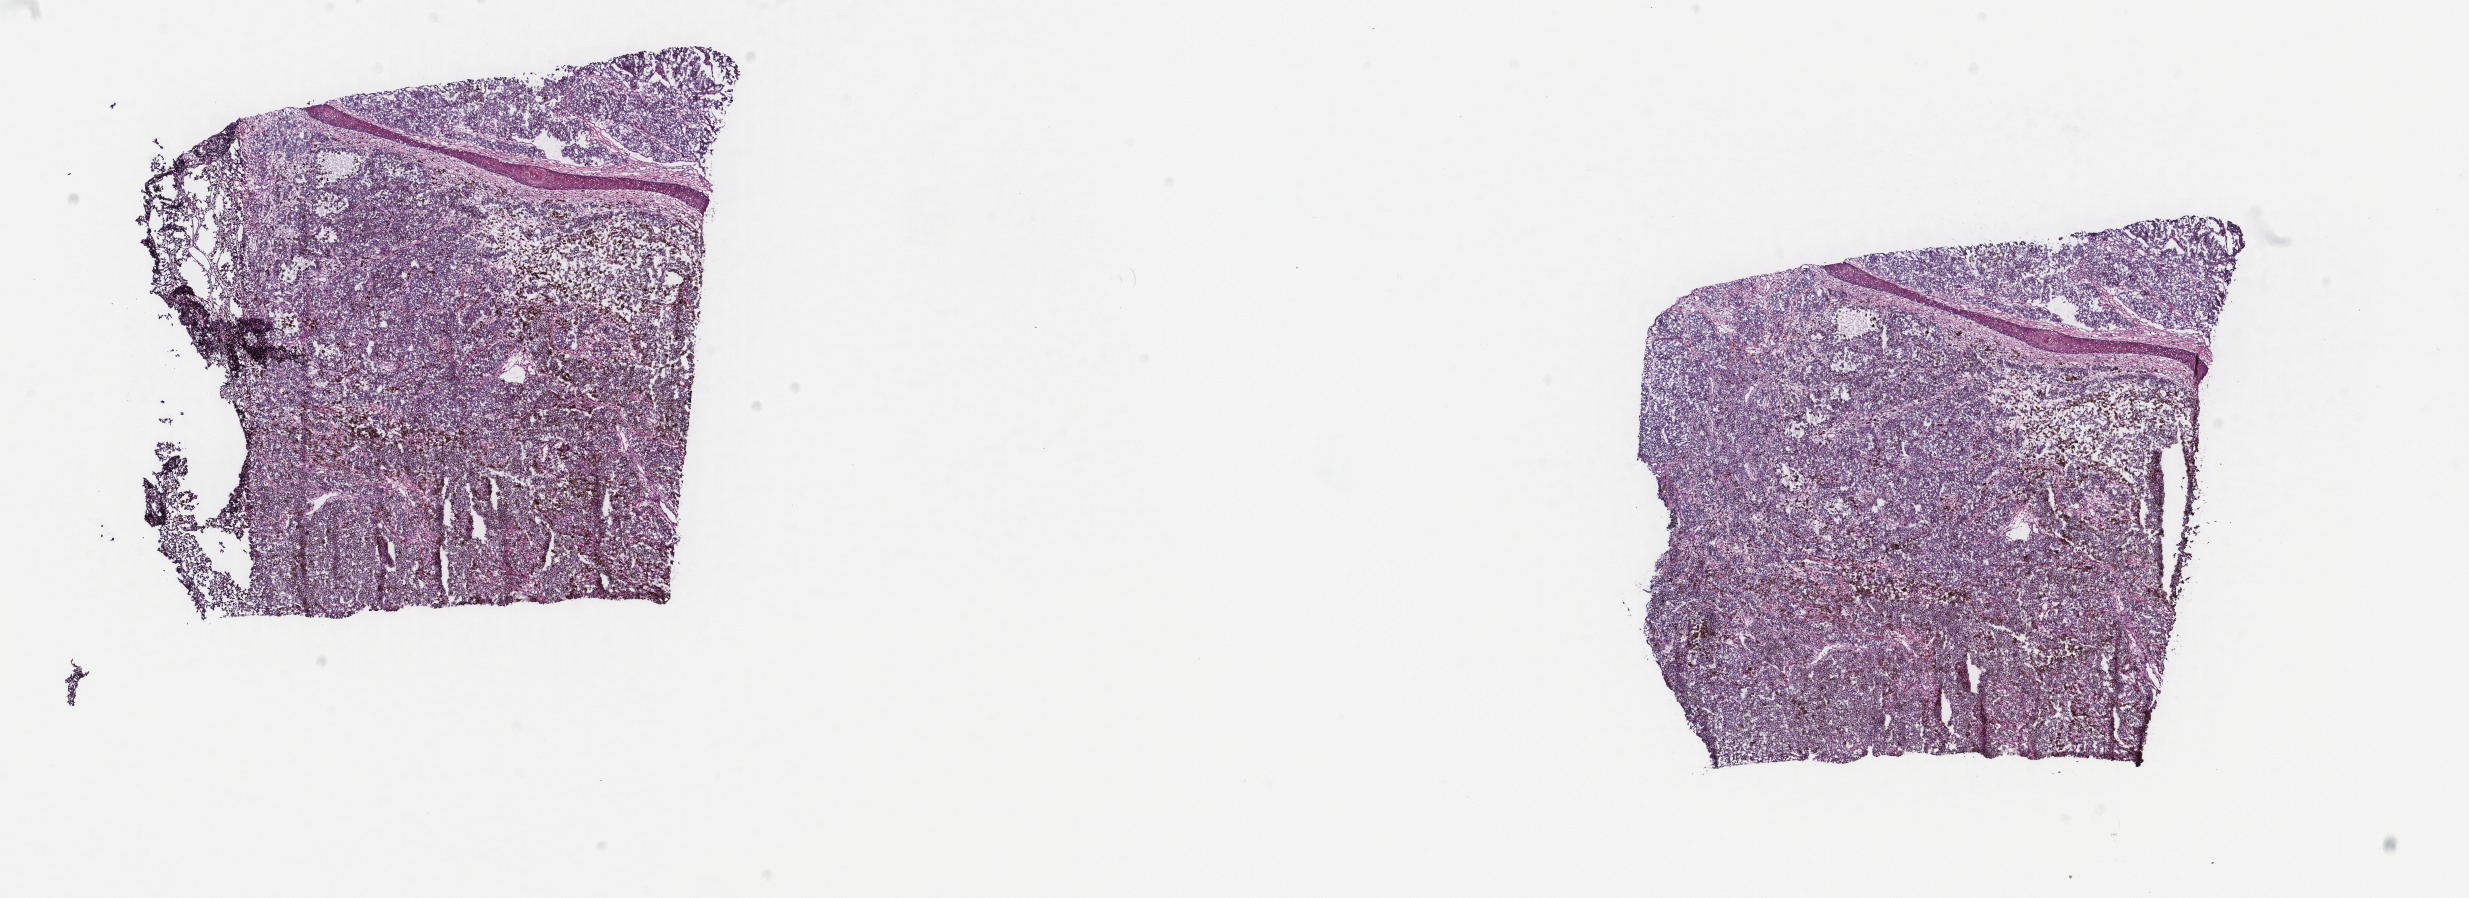
Hematoxylin and eosin (H&E) stained whole-slide image — whole scanned area (about 19.6 x 7.1 mm, slide scanned at 40x) shown as a low-resolution overview. Frozen section from the top of the tissue portion. Metastatic tumour sample, sampled site not recorded. Female patient; age at initial diagnosis 84 years. Pathologist review of this section (percent, as recorded): tumour cells 85%, tumour nuclei 85%, normal cells 0%, stromal cells 13%, necrosis 2%. Infiltration values recorded for this section: lymphocyte infiltration 1%, monocyte infiltration 1%, neutrophil infiltration 0%.
This section: metastatic tumour tissue. Patient diagnosis: Malignant melanoma, NOS.